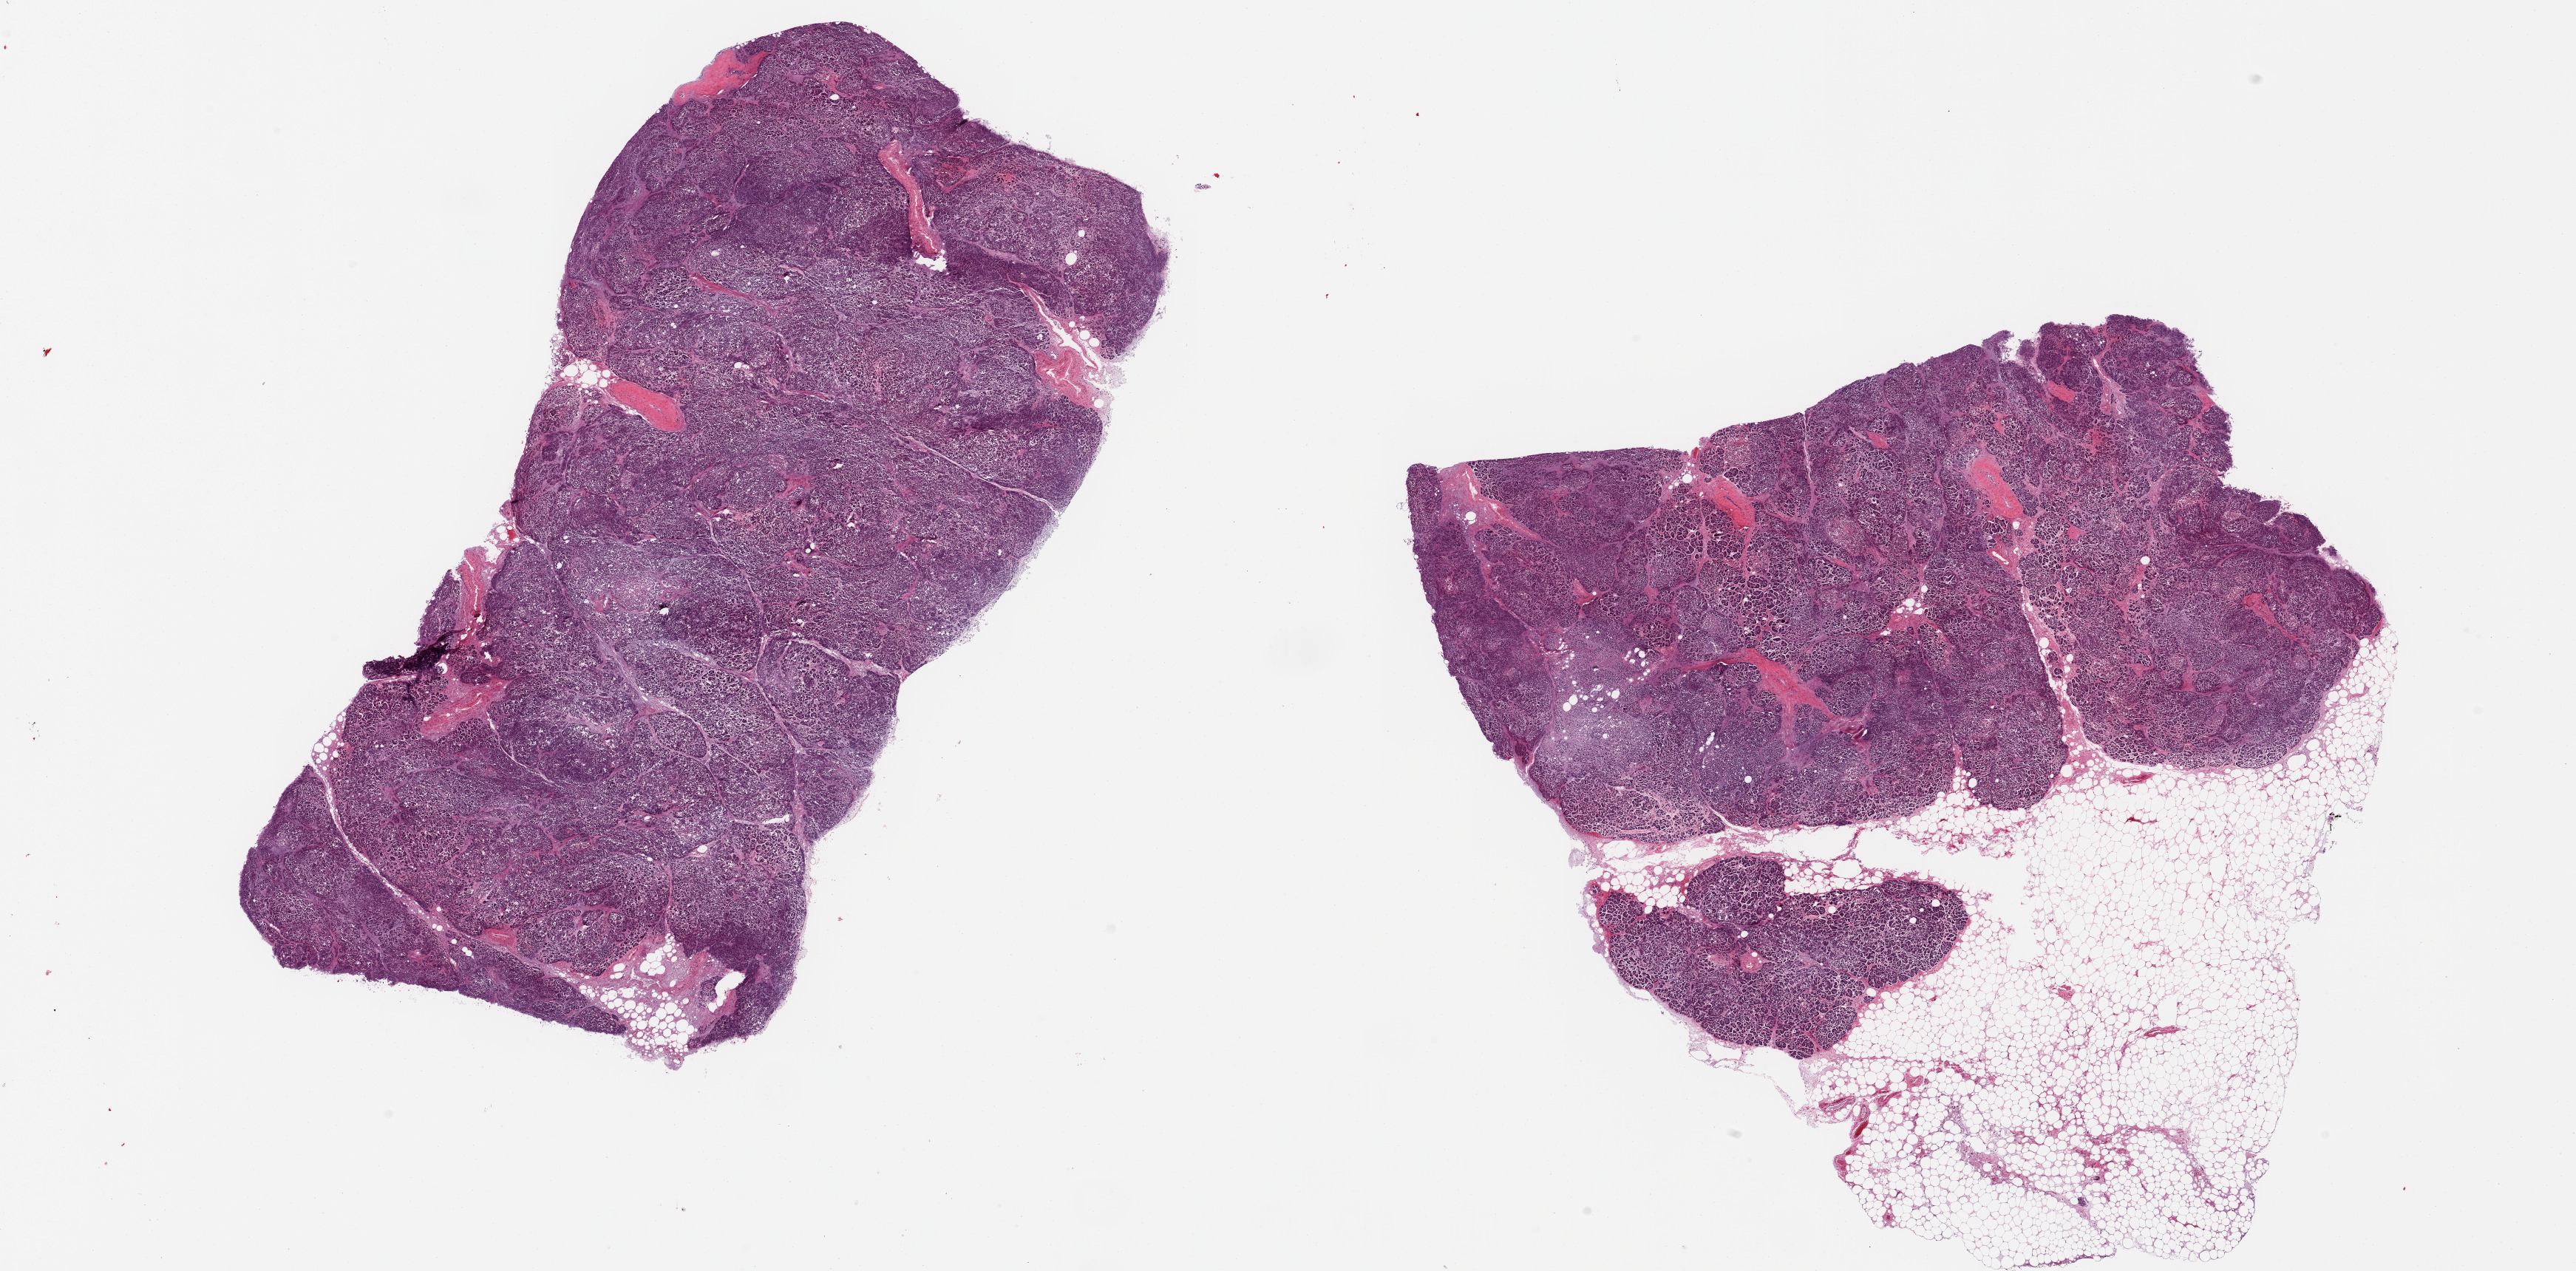
H&E whole-slide image, brightfield, low-resolution overview of the scanned area, about 27.6 x 13.6 mm; PAXgene-fixed paraffin-embedded (PFPE) section; target tissue: pancreas; tissue donor sample. Donor: male.
Reviewer comment on this tissue sample: 2 pieces; 1 with 40% external fat; tissue dissociated.